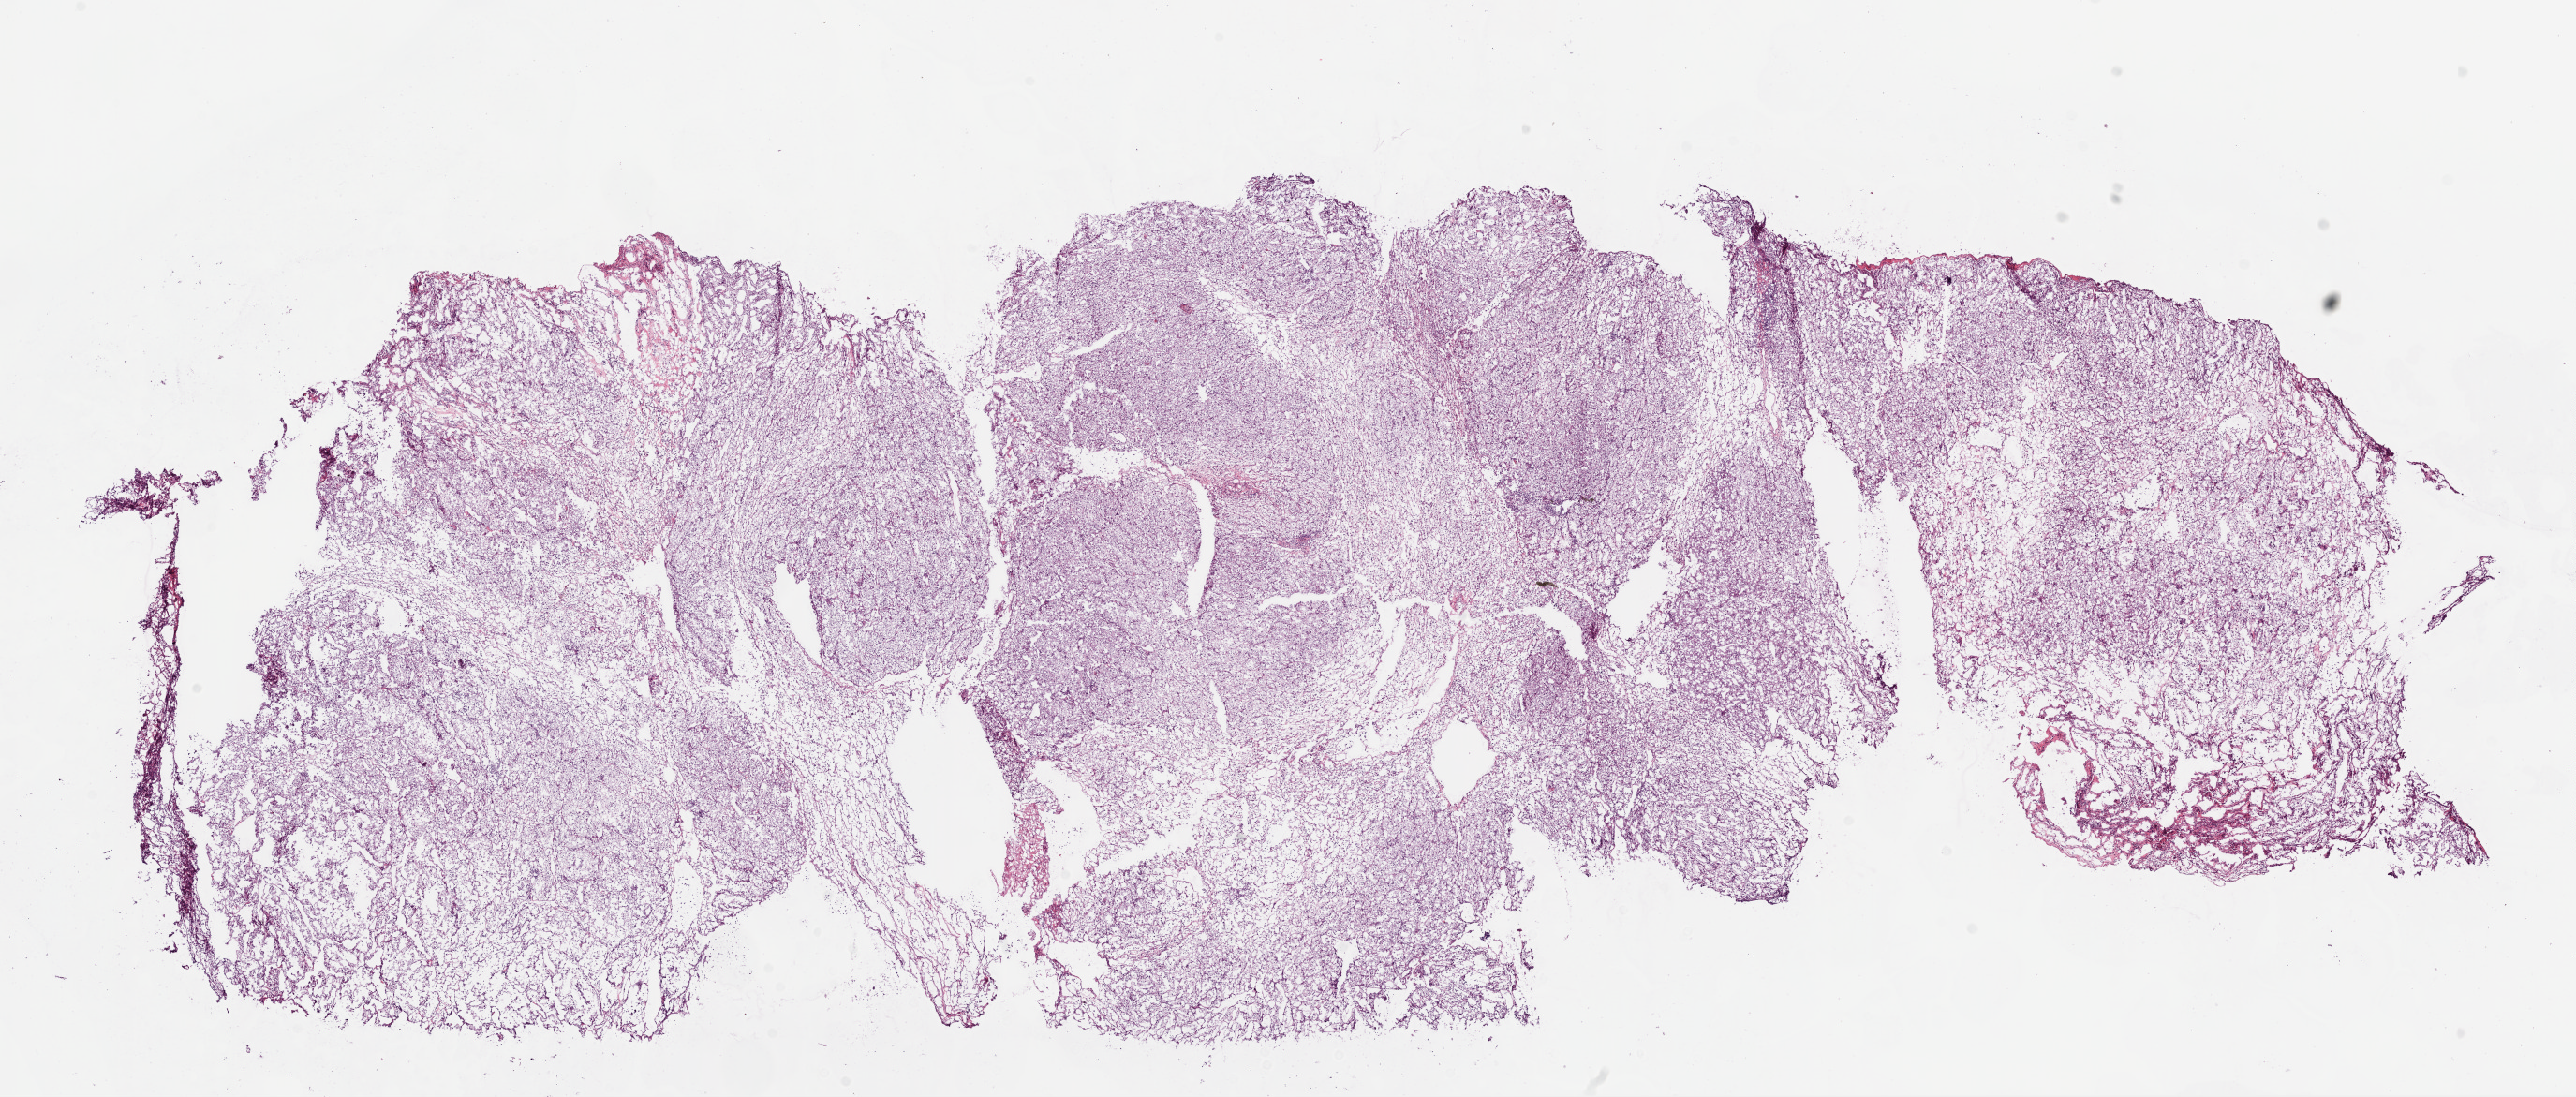
Digitized H&E tissue section (whole slide), low-resolution overview of the scanned area, about 22.1 x 9.4 mm (acquisition: 20x scan). Frozen section from the bottom of the tissue portion. Primary tumour sample from the kidney. Patient: female, age at initial diagnosis 69 years. Histologic grade: G3 (poorly differentiated). Composition of this section per pathologist review: tumour cells 90%, tumour nuclei 85%, normal cells 0%, stromal cells 10%, necrosis 0%.
AJCC pathologic stage: III. Pathologic diagnosis: Clear cell adenocarcinoma, NOS. Laterality: right. TNM: T3a NX M0.